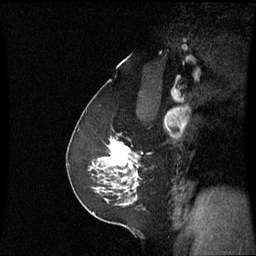
Breast MRI (dynamic contrast-enhanced), one sagittal slice; slice 40 of 60 in the series (ordered by position); dynamic contrast-enhanced series, image 2 of 3 at this slice position (ordered by acquisition); 1.5 T; TE 4.2 ms, TR 8.9 ms; 2.2 mm slice thickness; 256 × 256 image matrix, field of view 220 × 220 mm. Female patient, age 58 years. From the clinical record (not read from this slice): setting: breast cancer imaged before/during neoadjuvant chemotherapy; receptor status: triple-negative.
Annotated regions visible in this slice (semi-automatic segmentation, software-assisted and operator-edited):
- analysis volume of interest (the breast-tissue region the enhancement analysis was run in; not a lesion): bounding box (x1, y1, x2, y2) in pixels: (90, 138, 141, 193)
- tumour enhancement mask (voxels above the 70 % enhancement threshold inside the analysis volume of interest): (104, 140, 139, 187)